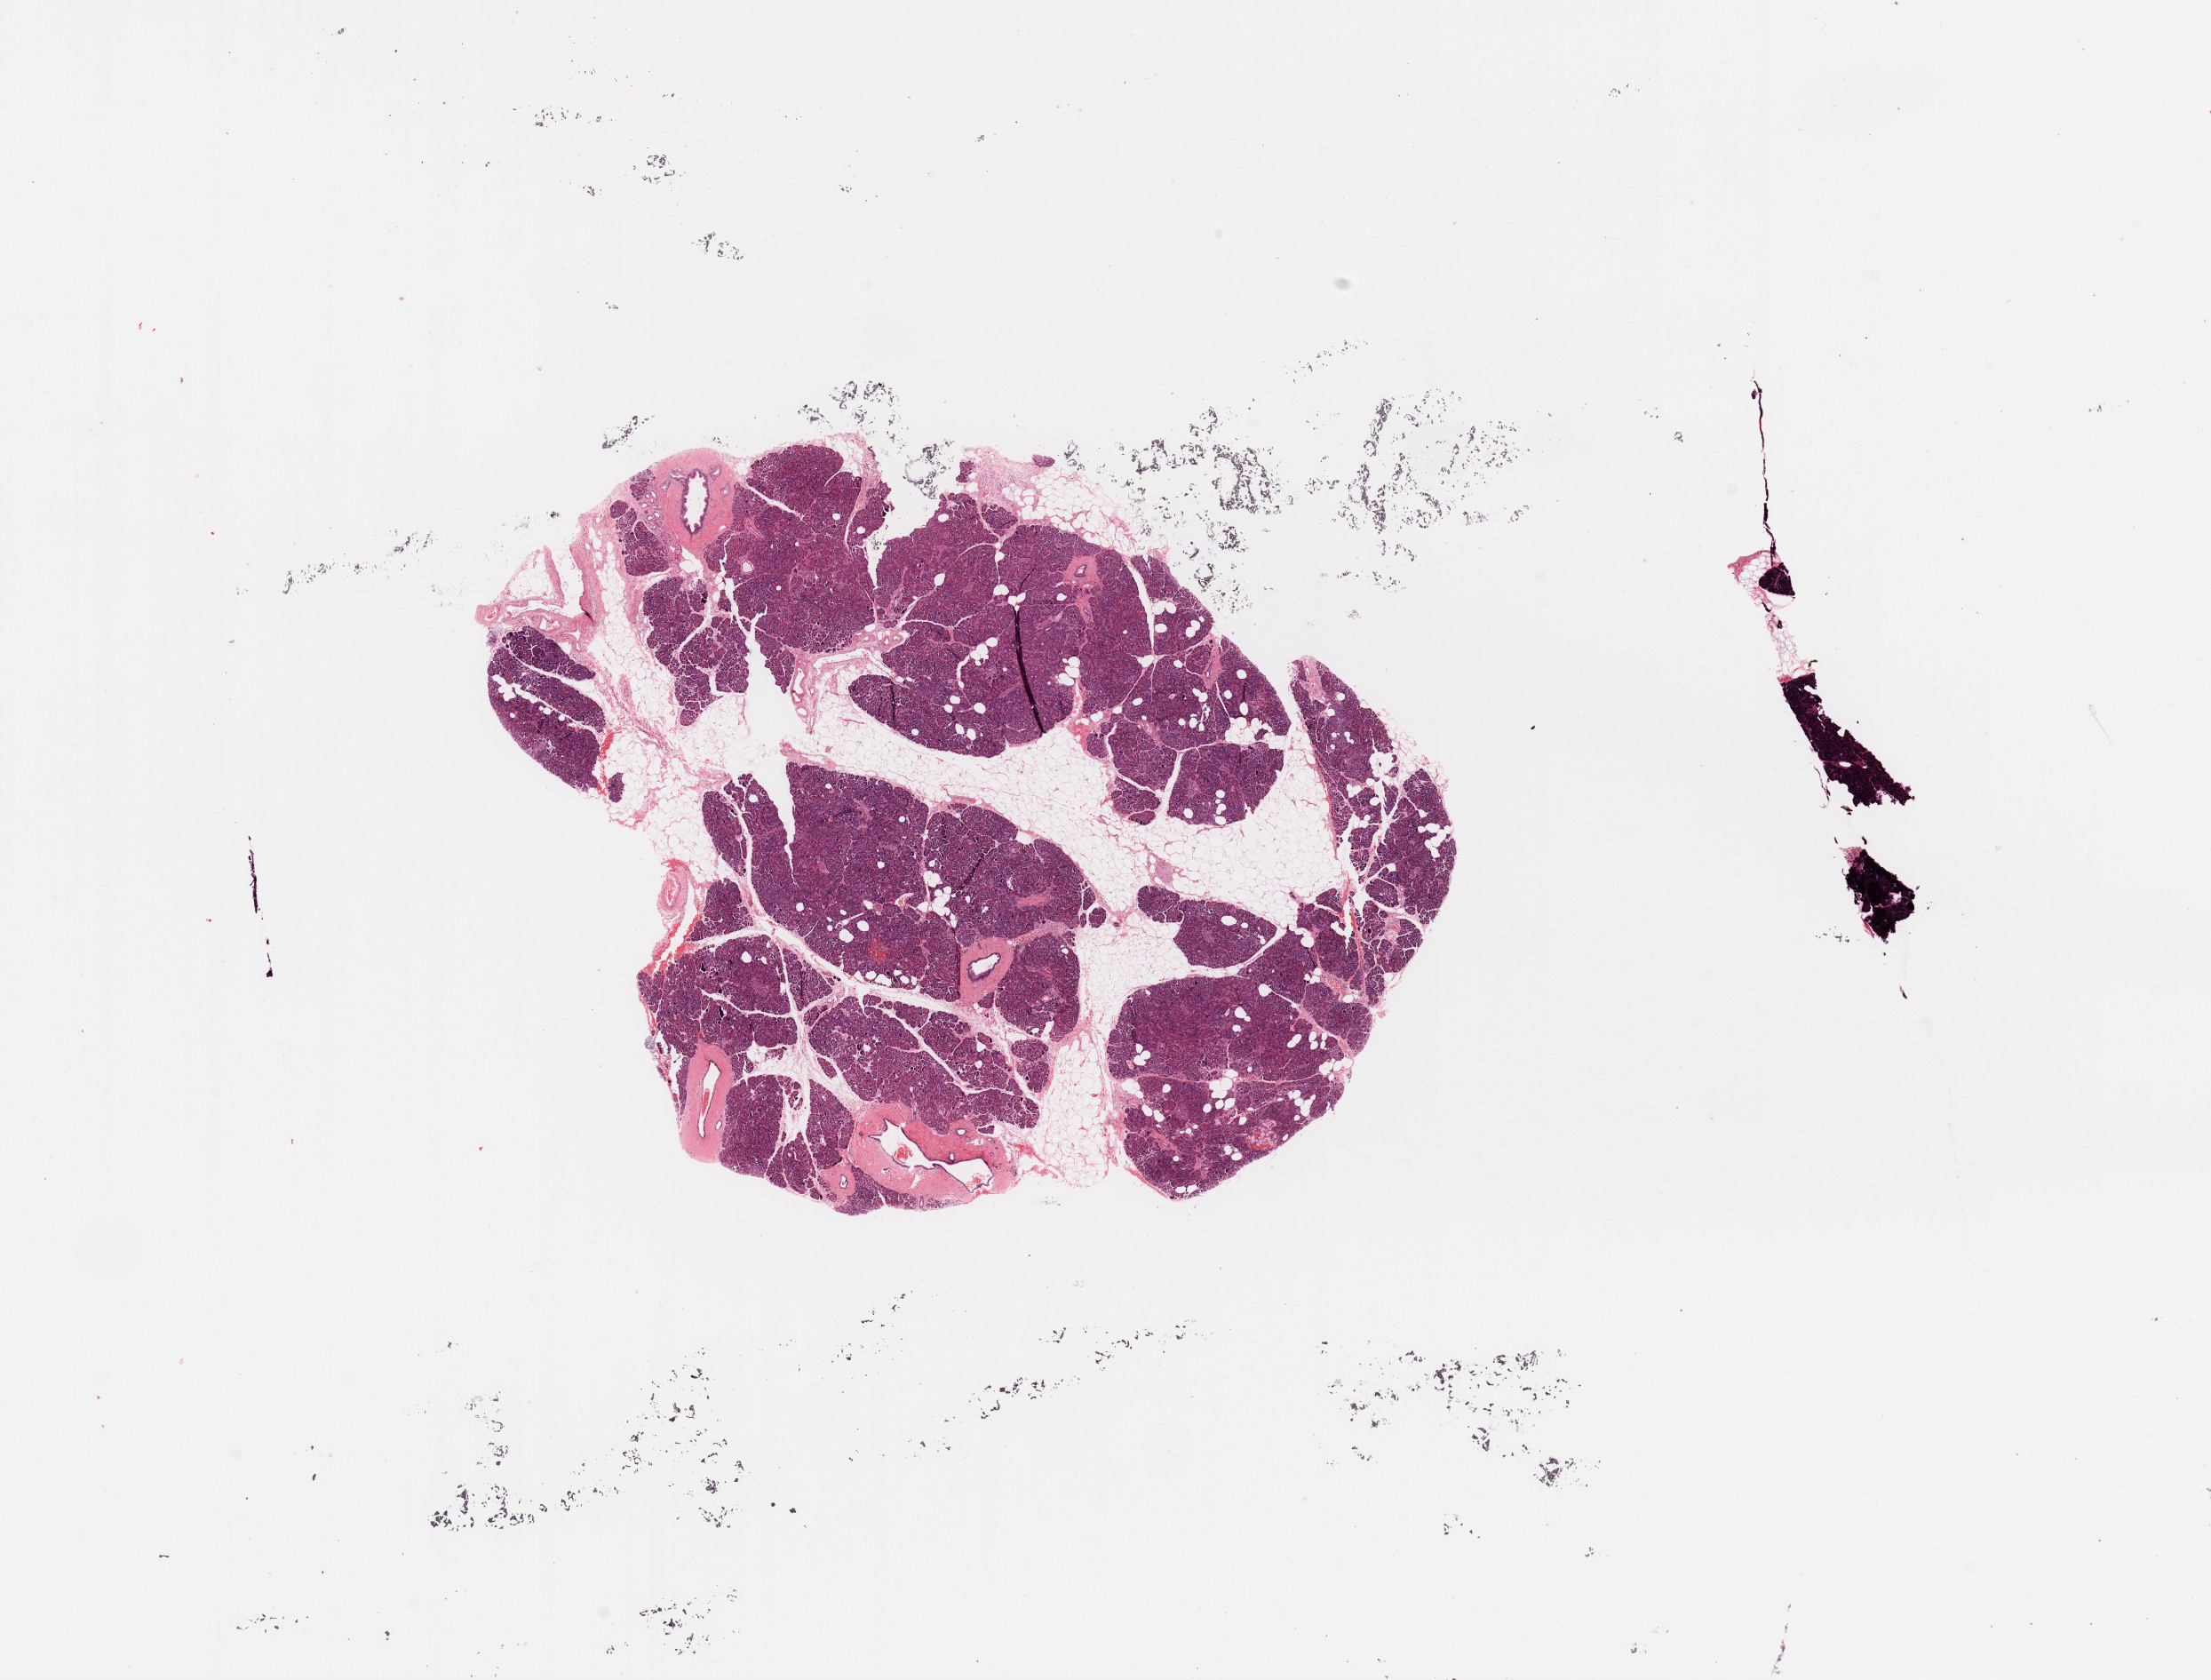
Digitized H&E-stained tissue section (whole slide), low-resolution overview of the scanned area, about 19.7 x 15.0 mm (slide scanned at 20x), normal (non-tumour) tissue sample, sampled site: pancreas. Patient: male, age 65 years.
This section: normal (non-tumour) tissue from the same patient. Patient diagnosis: Infiltrating duct carcinoma, NOS.